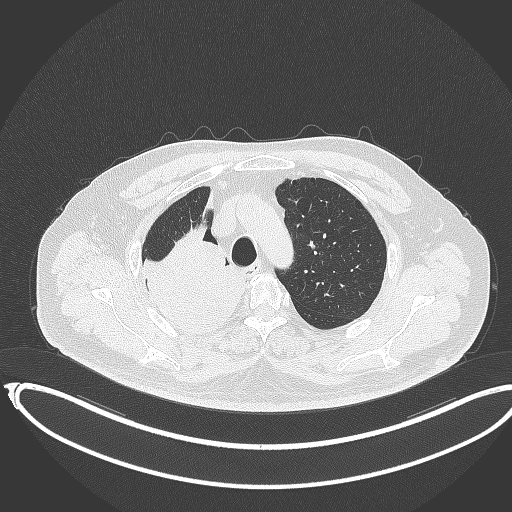
Chest CT, one axial slice; position 287 of 403 along the scan axis; 120 kVp; lung window (W 1500 / L -600 HU); 1 mm slice thickness; 512 × 512 image matrix, field of view 436 × 436 mm. Patient: male, 68 years. From the clinical record (not read from this slice): clinical TNM (as recorded): T2a N0 M0.
Structures marked on this image (rectangle marked by the reading radiologist):
- lung tumour (recorded histology: adenocarcinoma): bounding box [x1, y1, x2, y2] px = [134, 223, 244, 336]